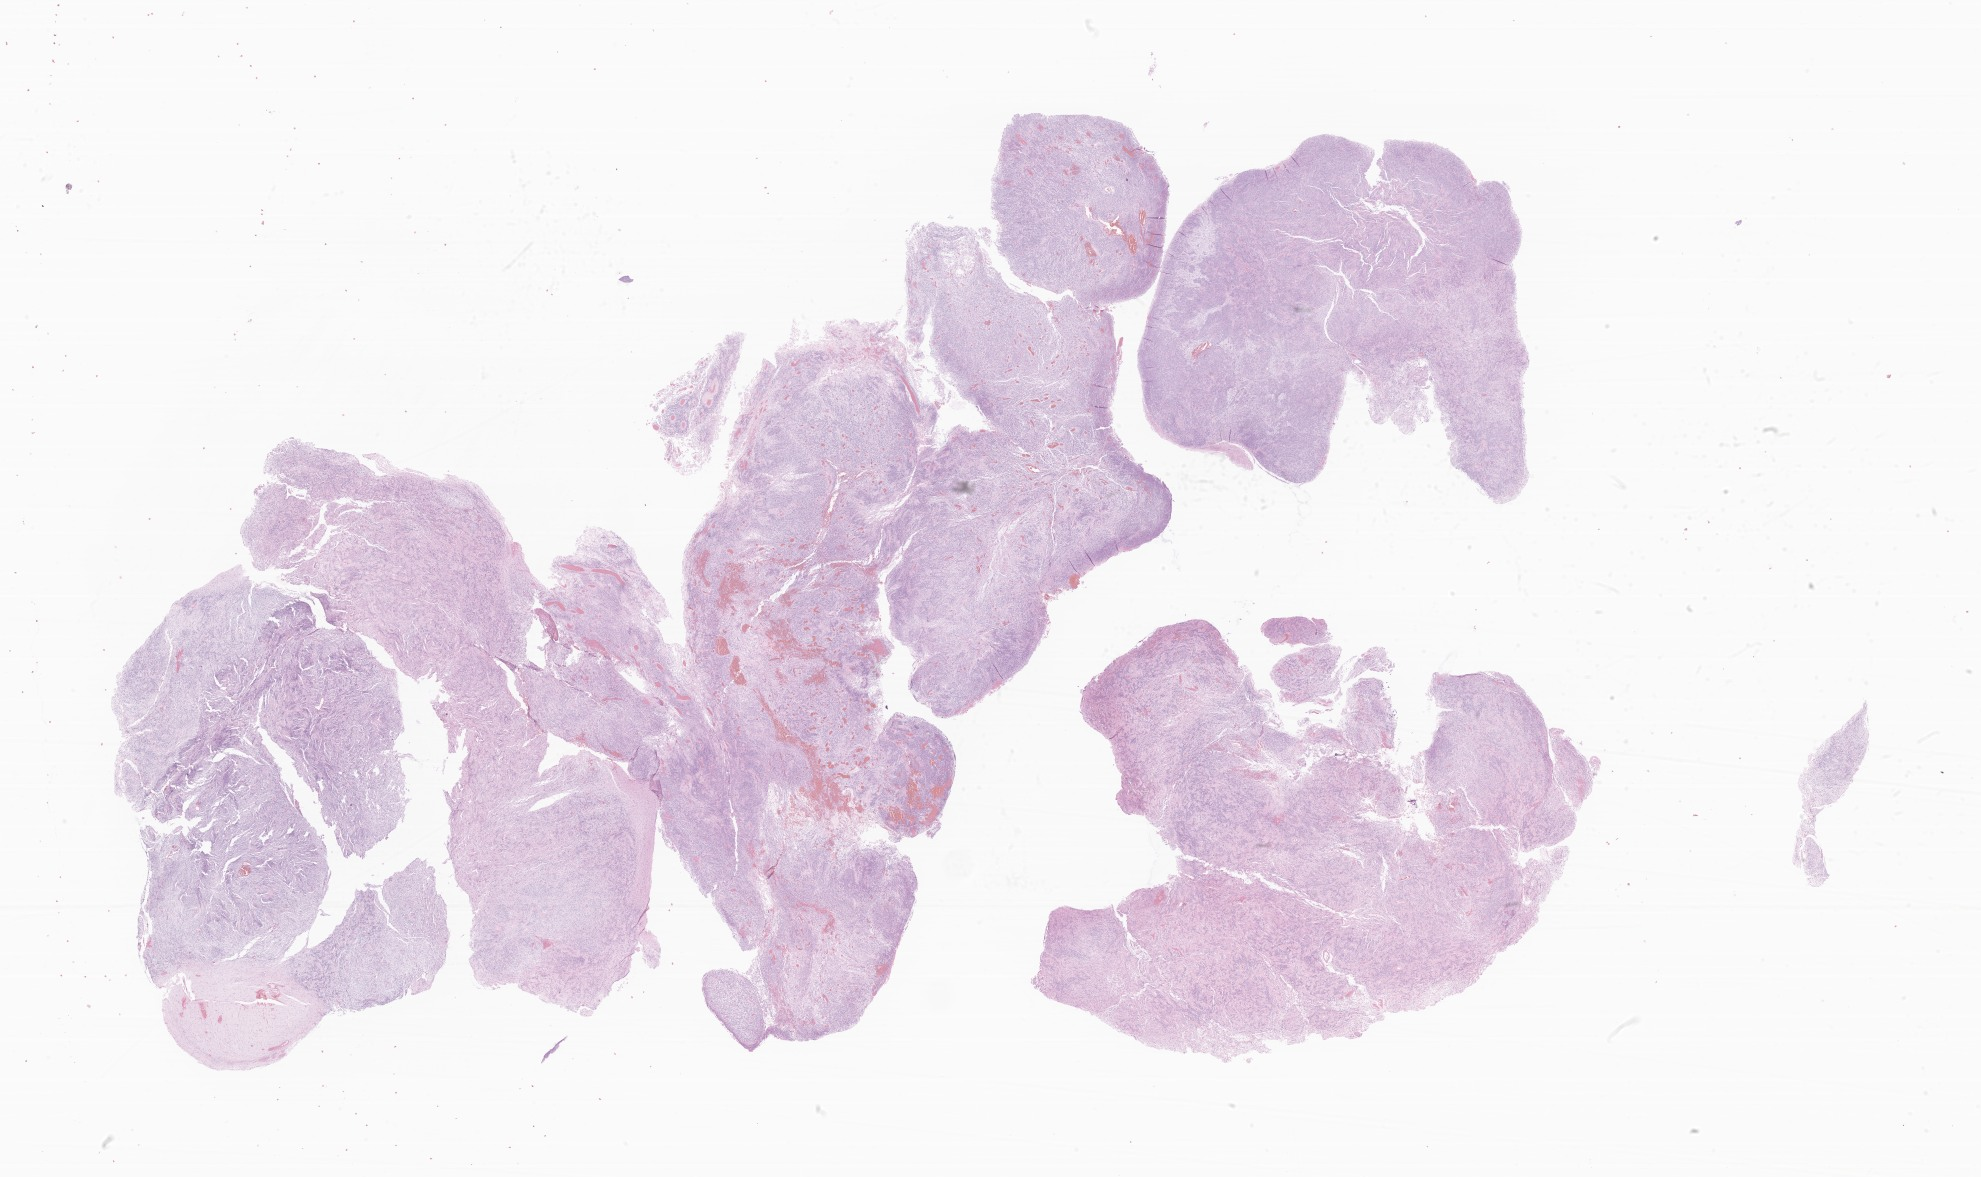
Whole-slide image, hematoxylin and eosin (H&E) stain of tumor tissue from the cerebrum — whole scanned area (about 33.4 x 19.9 mm) shown as a low-resolution overview. FFPE section. Patient: female, age 118 months (9 years 10 months).
Diagnosis (ICD-O-3 morphology term): Ependymoma, anaplastic.